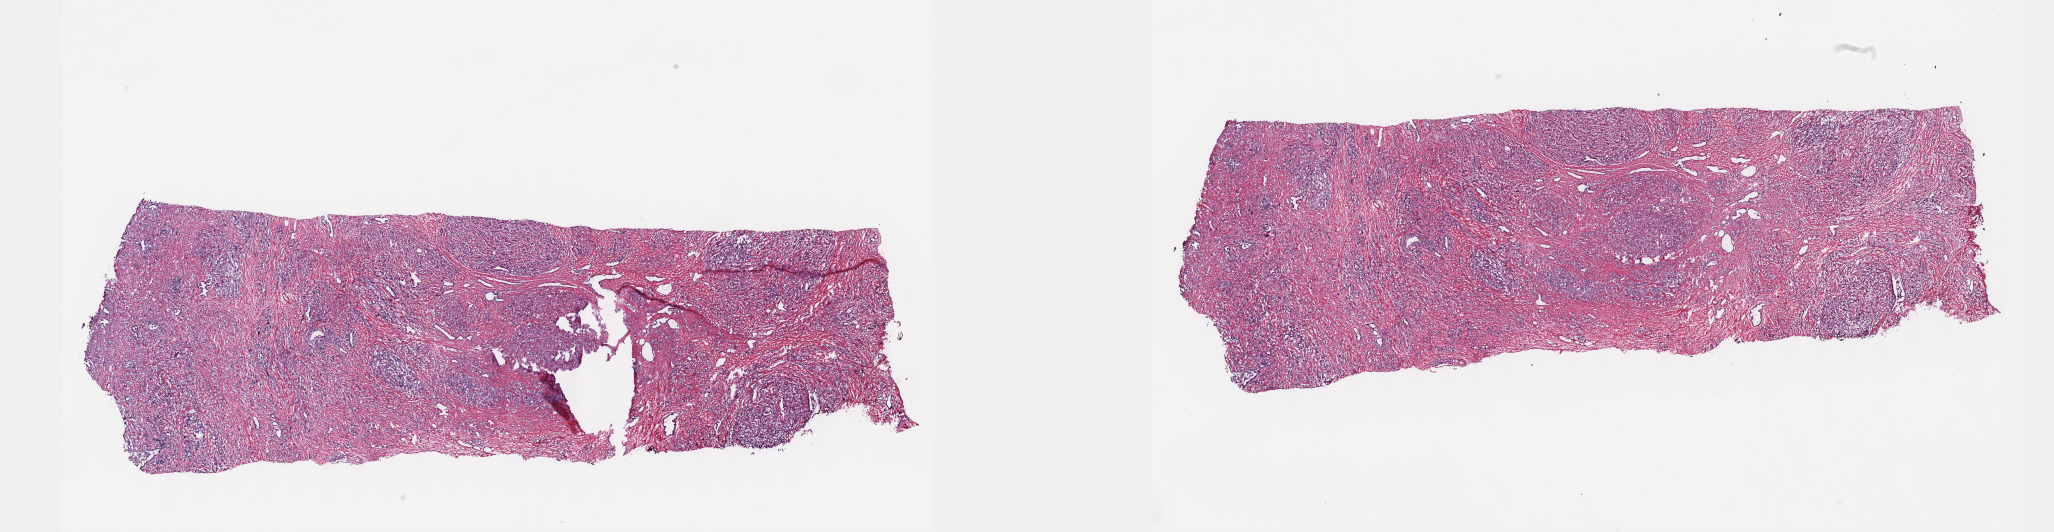
Hematoxylin and eosin (H&E) stained whole-slide image, shown as a low-resolution overview of the whole scanned area (about 33.2 x 8.6 mm), frozen section from the top of the tissue portion, prostate, primary tumour sample. Male patient; age at initial diagnosis 60 years. Gleason score: 9 (4+5). Pathologist review of this section (percent, as recorded): tumour cells 70%, tumour nuclei 80%, normal cells 0%, stromal cells 30%, necrosis 0%. Inflammatory infiltration, as recorded: lymphocyte infiltration 0%, monocyte infiltration 0%, neutrophil infiltration 0%.
- laterality: bilateral
- pathologic diagnosis: Adenocarcinoma, NOS (prostate gland)
- lymph nodes positive (case pathology): 0 of 29 examined